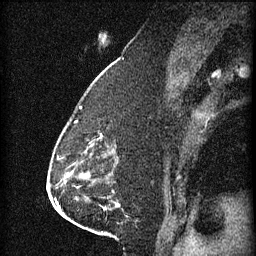
Breast MRI (dynamic contrast-enhanced), one sagittal slice. Slice 32 of 60 in the series (ordered by position). 3 images stored at this slice position (order not interpretable as contrast timing). 1.5 T. TE 4.2 ms, TR 11 ms. 256 × 256 image matrix, field of view 180 × 180 mm. Female patient, age 63 years.
Outlined on this slice (semi-automatic segmentation, software-assisted and operator-edited):
- analysis volume of interest (the breast-tissue region the enhancement analysis was run in; not a lesion): bounding box (x1, y1, x2, y2) in pixels: (86, 118, 117, 153)
- tumour enhancement mask (voxels above the 70 % enhancement threshold inside the analysis volume of interest): (90, 134, 103, 147)